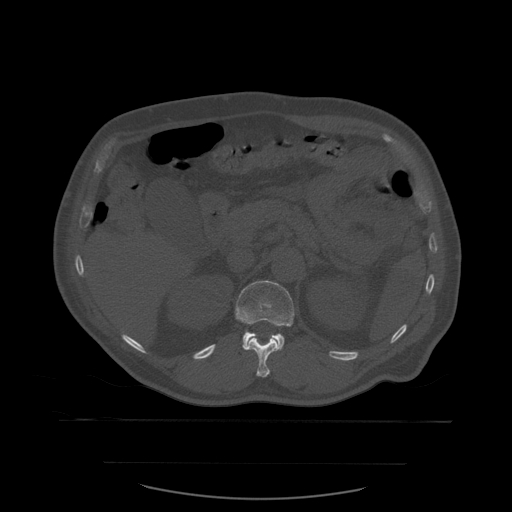
CT including the spine, one axial slice. Bone window (W 1800 / L 400 HU). 1.25 mm slice thickness. 512 × 512 image matrix, field of view 479 × 479 mm. Patient age 71 years. From the clinical record (not read from this slice): primary cancer: lung; vertebrae with lytic lesions (as recorded): T1, T2, L5, S1.
Structures marked on this image (semi-automatic segmentation, software-assisted and operator-edited):
- L1 vertebra: bounding box (x1, y1, x2, y2) in pixels: (235, 281, 295, 350)
- T12 vertebra: (242, 335, 281, 378)